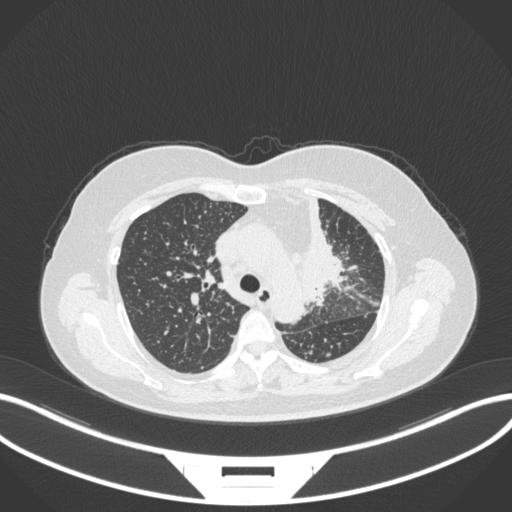
Chest CT, one axial slice. Slice 236 of 348 in the series (ordered by position). Reconstruction kernel B31f. Lung window (W 1500 / L -600 HU). 512 × 512 image matrix. Patient: female, 49 years. From the clinical record (not read from this slice): clinical TNM (as recorded): T1c N0 M1.
Structures marked on this image (bounding box drawn by a radiologist):
- lung tumour (recorded histology: adenocarcinoma): bounding box (x1, y1, x2, y2) in pixels: (298, 191, 351, 308)